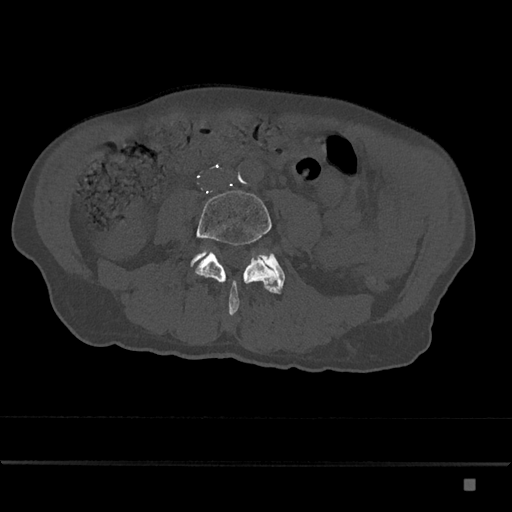
CT including the spine, one axial slice; reconstruction kernel Br40s/3; bone window (W 1800 / L 400 HU); 0.5 mm slice thickness; 512 × 512 image matrix, field of view 390 × 390 mm. Male patient, age 72 years. From the clinical record (not read from this slice): primary cancer: prostate.
Annotated regions visible in this slice (semi-automatically segmented with operator editing):
- L4 vertebra: bounding box [x1, y1, x2, y2] px = [191, 190, 278, 315]
- L5 vertebra: [191, 249, 285, 294]